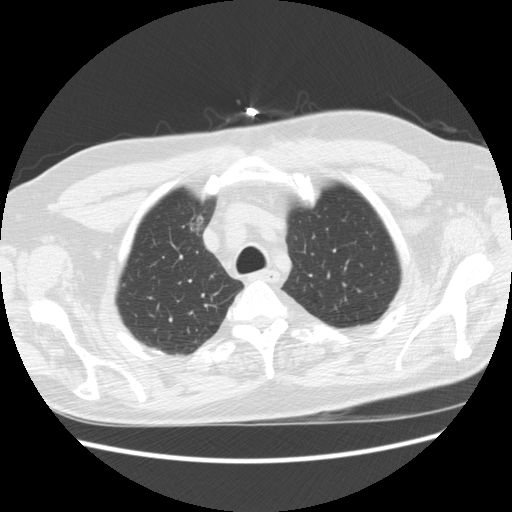
Low-dose screening chest CT, axial slice, baseline screening round, lung window (W 1500 / L -600 HU). Male, age 66 years at enrolment. Former smoker at enrolment.
- Expert-annotated lung lesion, bounding box [x1, y1, x2, y2] px = [167, 208, 213, 242].
- Screening reader's record for this exam: no non-calcified nodule ≥4 mm recorded.
- Participant outcome: lung cancer diagnosed 951 days after this screen — bronchiolo-alveolar adenocarcinoma, NOS, right upper lobe, moderately differentiated (G2), stage IA (AJCC 6th edition), 12 mm at pathology.